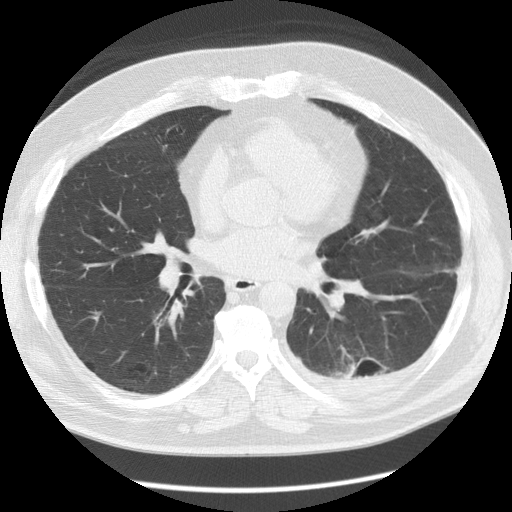
Low-dose screening chest CT, one axial slice; slice 64 of 126 in the series (ordered by position); reconstruction kernel STANDARD; 120 kVp; lung window (W 1500 / L -600 HU); 2.5 mm slice thickness; 512 × 512 image matrix, field of view 370 × 370 mm.
Annotated regions visible in this slice (outlined manually by an expert reader):
- lesion 1 (tumor, lower lobe of left lung): bounding box (x1, y1, x2, y2) in pixels: (344, 355, 364, 380)